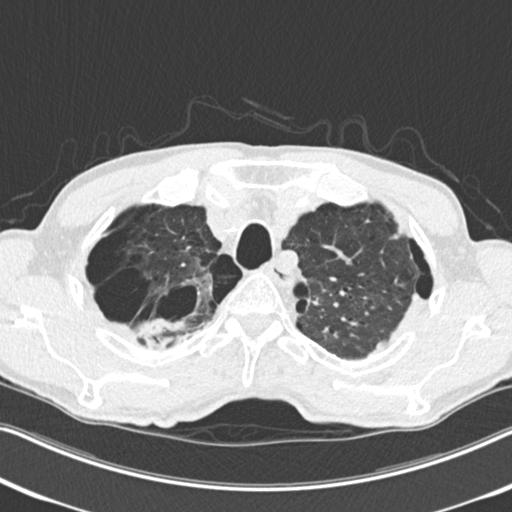
Low-dose screening chest CT, one axial slice; position 210 of 251 along the scan axis; reconstruction kernel B30f; 120 kVp; lung window (W 1500 / L -600 HU); 2 mm slice thickness; 512 × 512 image matrix, field of view 334 × 334 mm.
Outlined on this slice (expert manual segmentation):
- lesion 1 (tumor, upper lobe of right lung): box from (x=135, y=318) to (x=185, y=340) px